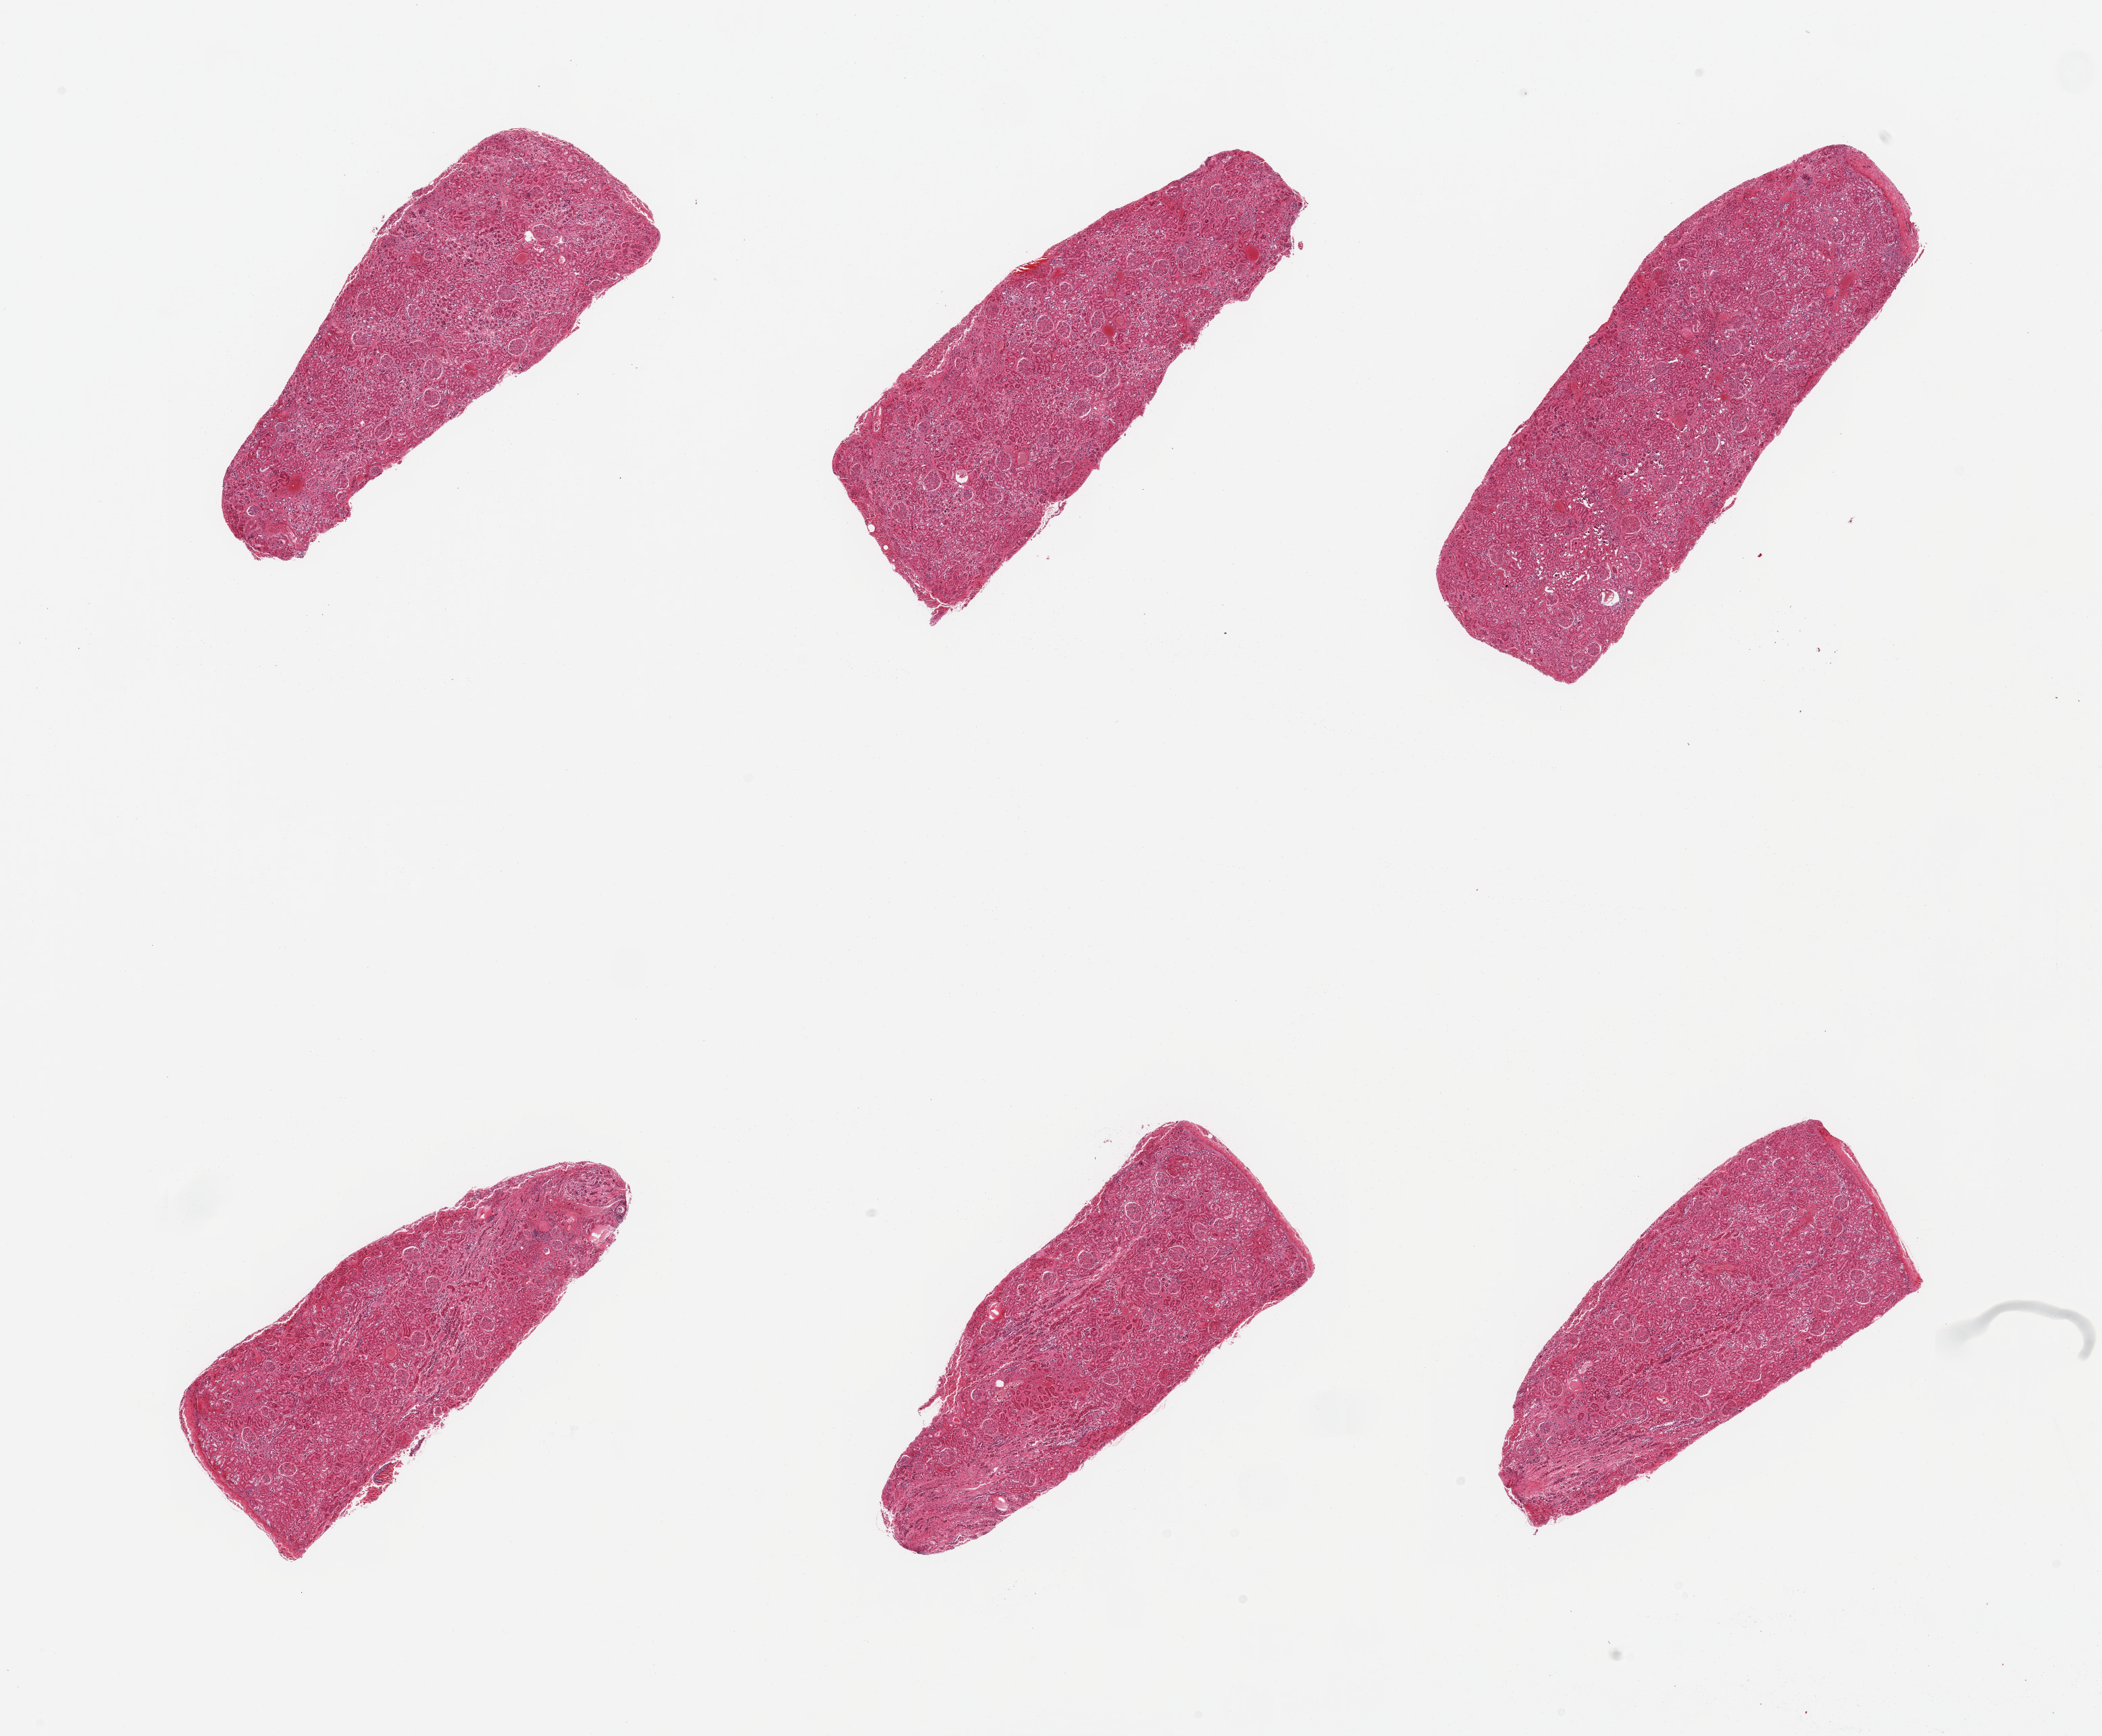
Digitized H&E-stained section — whole scanned area (about 24.6 x 20.3 mm, slide scanned at 20x) shown as a low-resolution overview. PAXgene-fixed paraffin-embedded (PFPE) section. Section of renal cortex (target tissue). Donor tissue sample. Male donor.
Pathologist's review note for this sample: 6 pieces, glomeruli present, all sections.